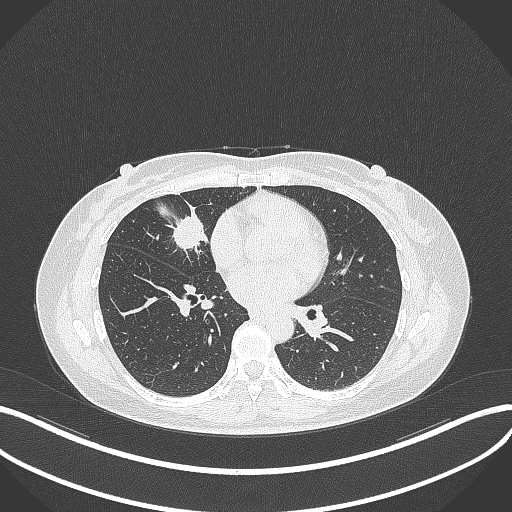
Chest CT, one axial slice; position 134 of 284 along the scan axis; lung window (W 1500 / L -600 HU); 1 mm slice thickness; 512 × 512 image matrix, field of view 400 × 400 mm. Patient: female, 43 years. From the clinical record (not read from this slice): clinical TNM (as recorded): T1c N3 M1; histopathological grade: G1.
Outlined on this slice (bounding box drawn by a radiologist):
- lung tumour (recorded histology: adenocarcinoma): bounding box [x1, y1, x2, y2] px = [166, 208, 208, 254]